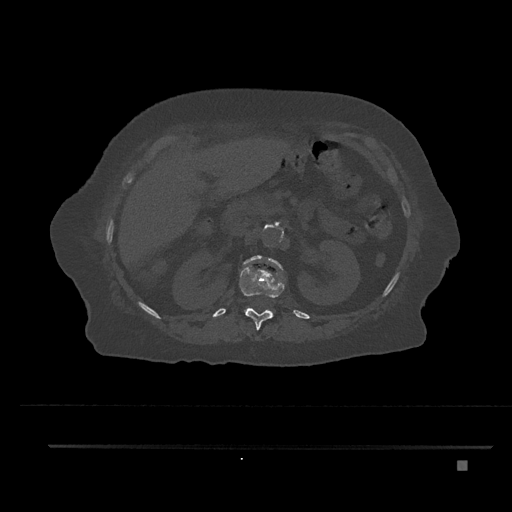
CT including the spine, one axial slice. Slice 251 of 797 in the series (ordered by position). Bone window (W 1800 / L 400 HU). 0.5 mm slice thickness. 512 × 512 image matrix, field of view 437 × 437 mm. Female patient, age 76 years. From the clinical record (not read from this slice): primary cancer: lung; vertebrae with lytic lesions (as recorded): T11, L3.
Structures marked on this image (semi-automatically segmented with operator editing):
- L1 vertebra: bounding box (x1, y1, x2, y2) in pixels: (243, 255, 285, 317)
- T12 vertebra: (239, 266, 285, 330)